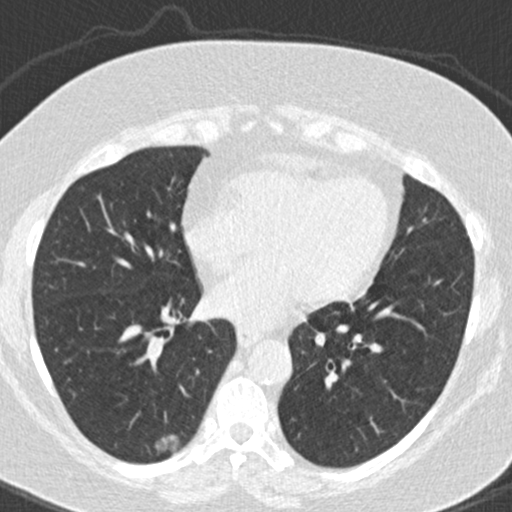
Axial slice from a low-dose chest CT screening exam. Baseline screening round. Lung window (W 1500 / L -600 HU). 2 mm slice thickness. Standard (soft-tissue) reconstruction kernel (B30f). Slice 105 of 177 in the series. Female participant, aged 63 years at enrolment.
• Expert reader's lesion annotation, bounding box (x1, y1, x2, y2) in pixels: (146, 426, 188, 463).
• The exam's reader record, not a measurement of the box and not confirmed to be the same lesion: non-calcified nodule or mass ≥4 mm, right lower lobe, 16 × 10 mm, poorly defined margins, ground glass attenuation.
• Official screen result: positive, change unspecified: nodule(s) >= 4 mm or enlarging nodule(s), mass(es), or other non-specific abnormalities suspicious for lung cancer.